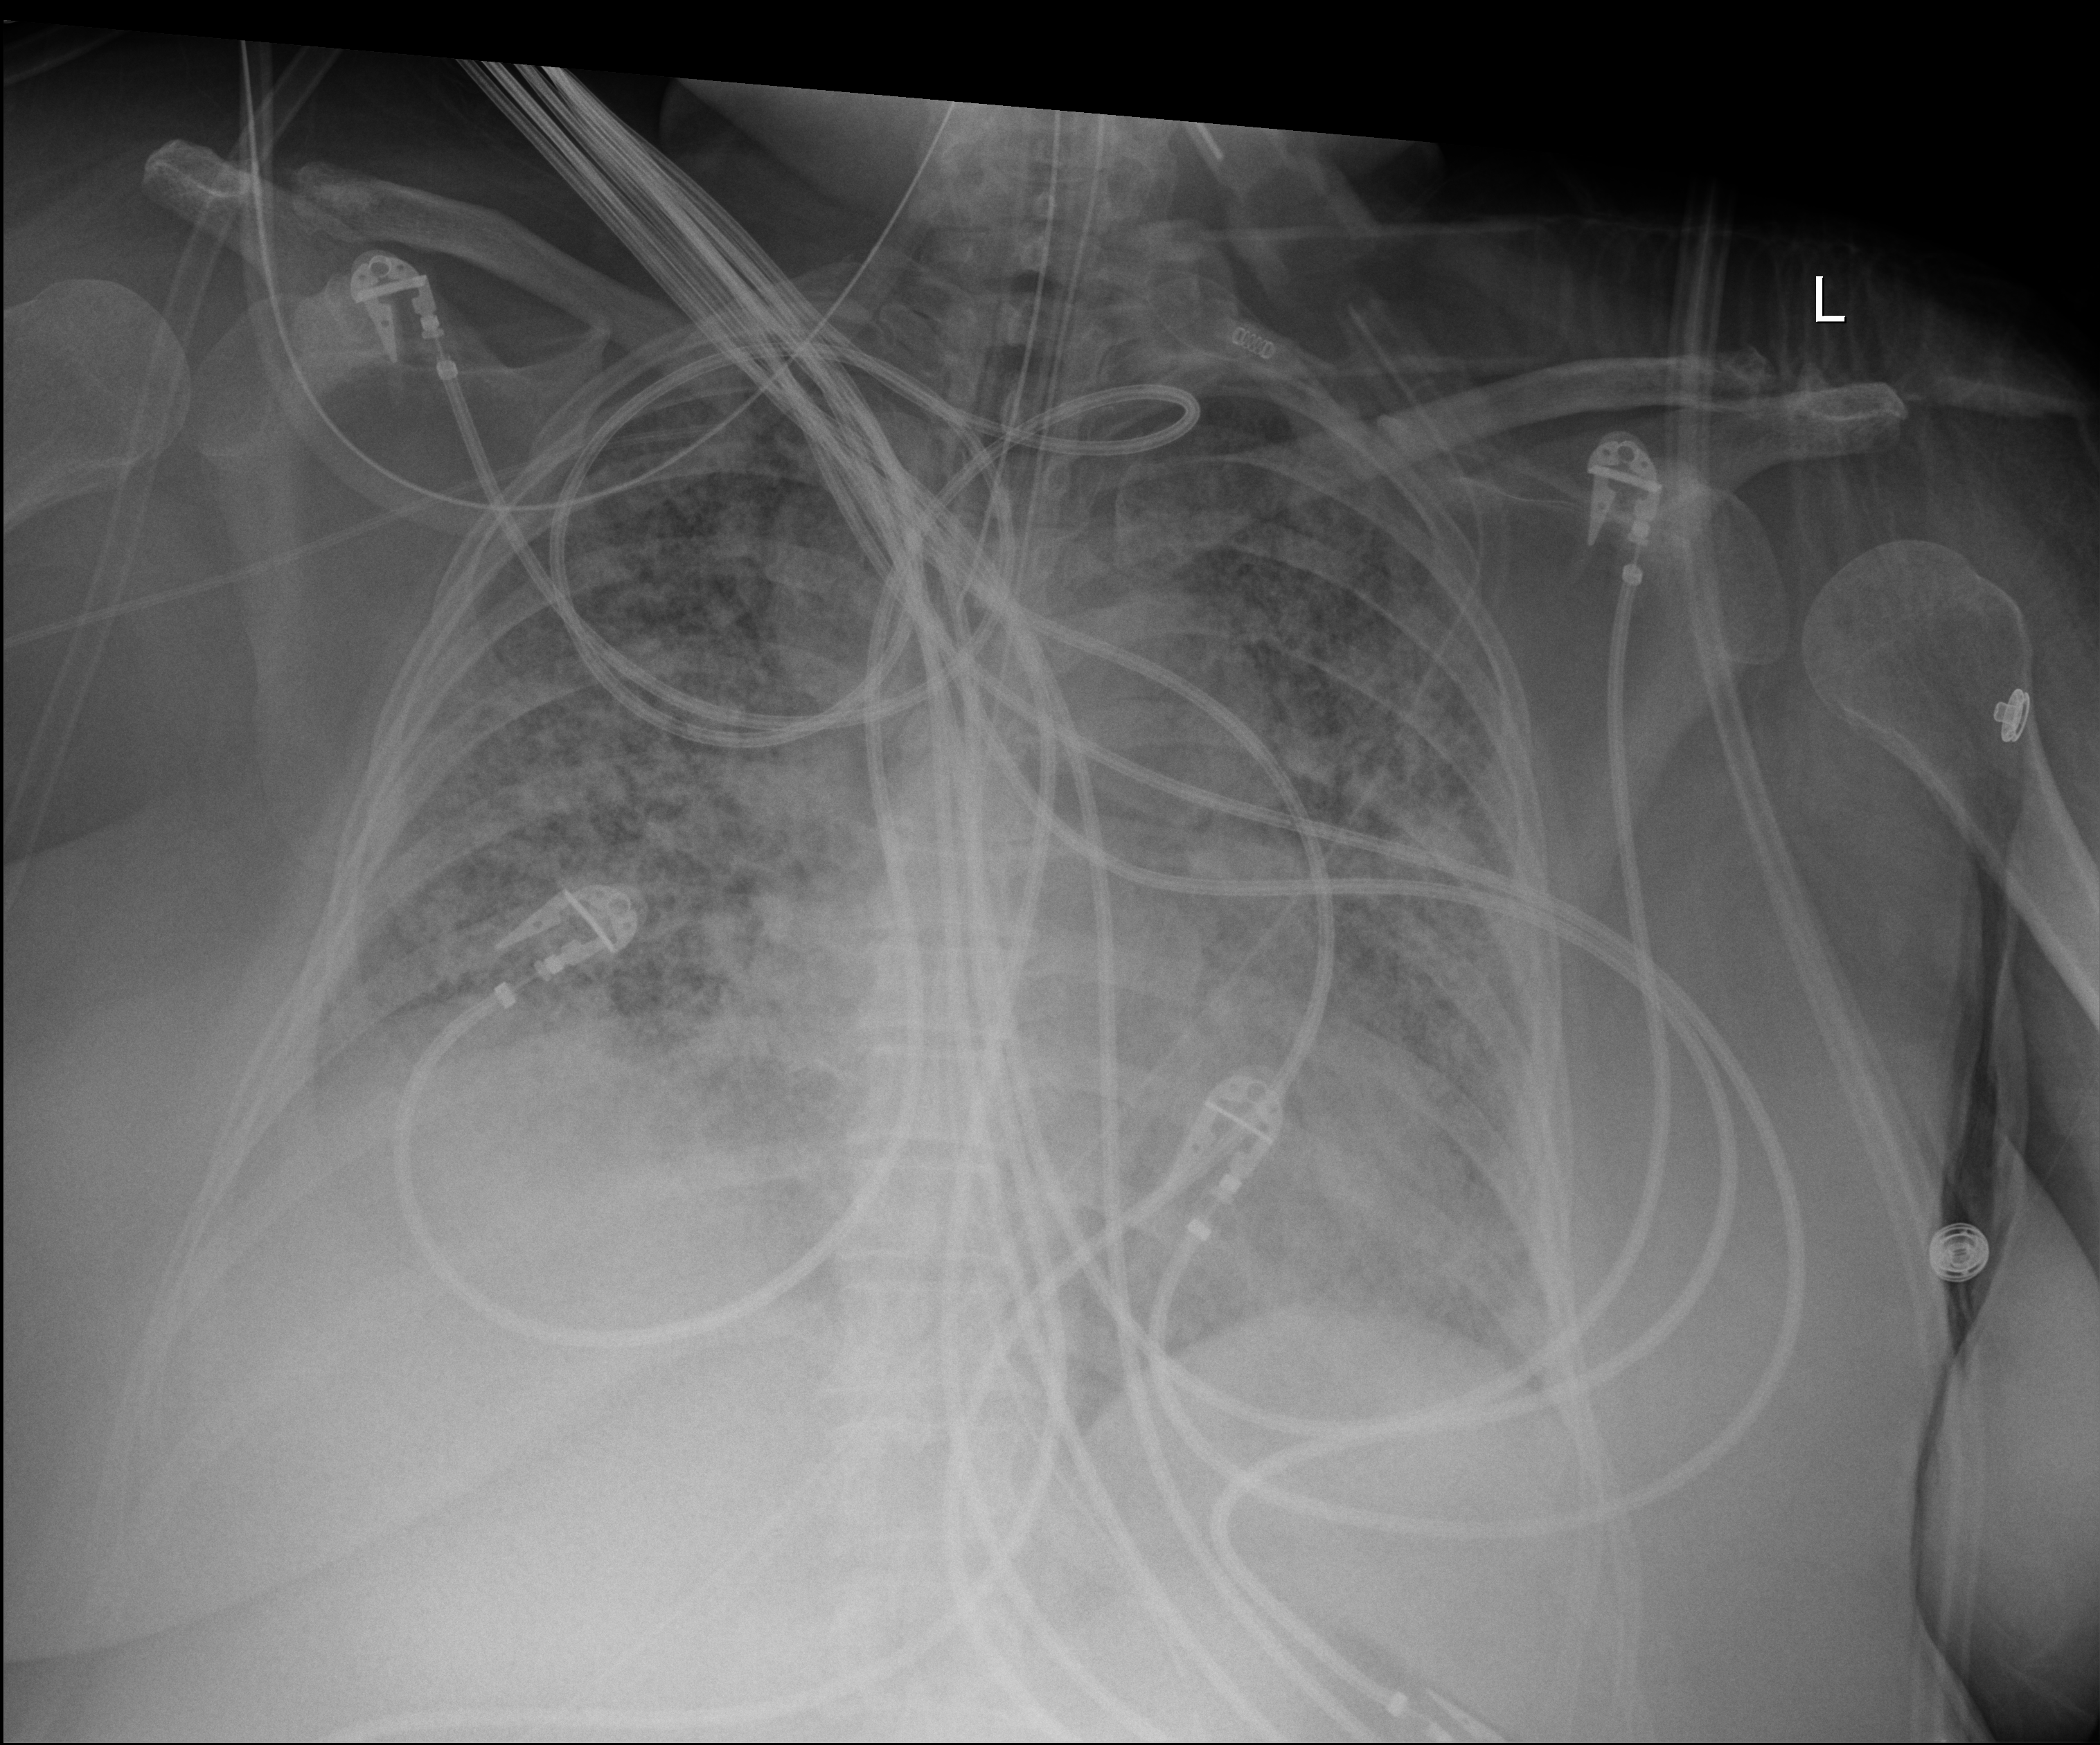
Chest radiograph (digital radiography); anteroposterior (AP) projection. Female patient hospitalised with COVID-19, age 18–59 years.
Hospital-stay facts (about this admission, not read from this image; timing relative to this image not recorded): other chronic lung disease (admission record): no; mechanically ventilated during this hospital stay: yes; length of hospital stay: 95 days.